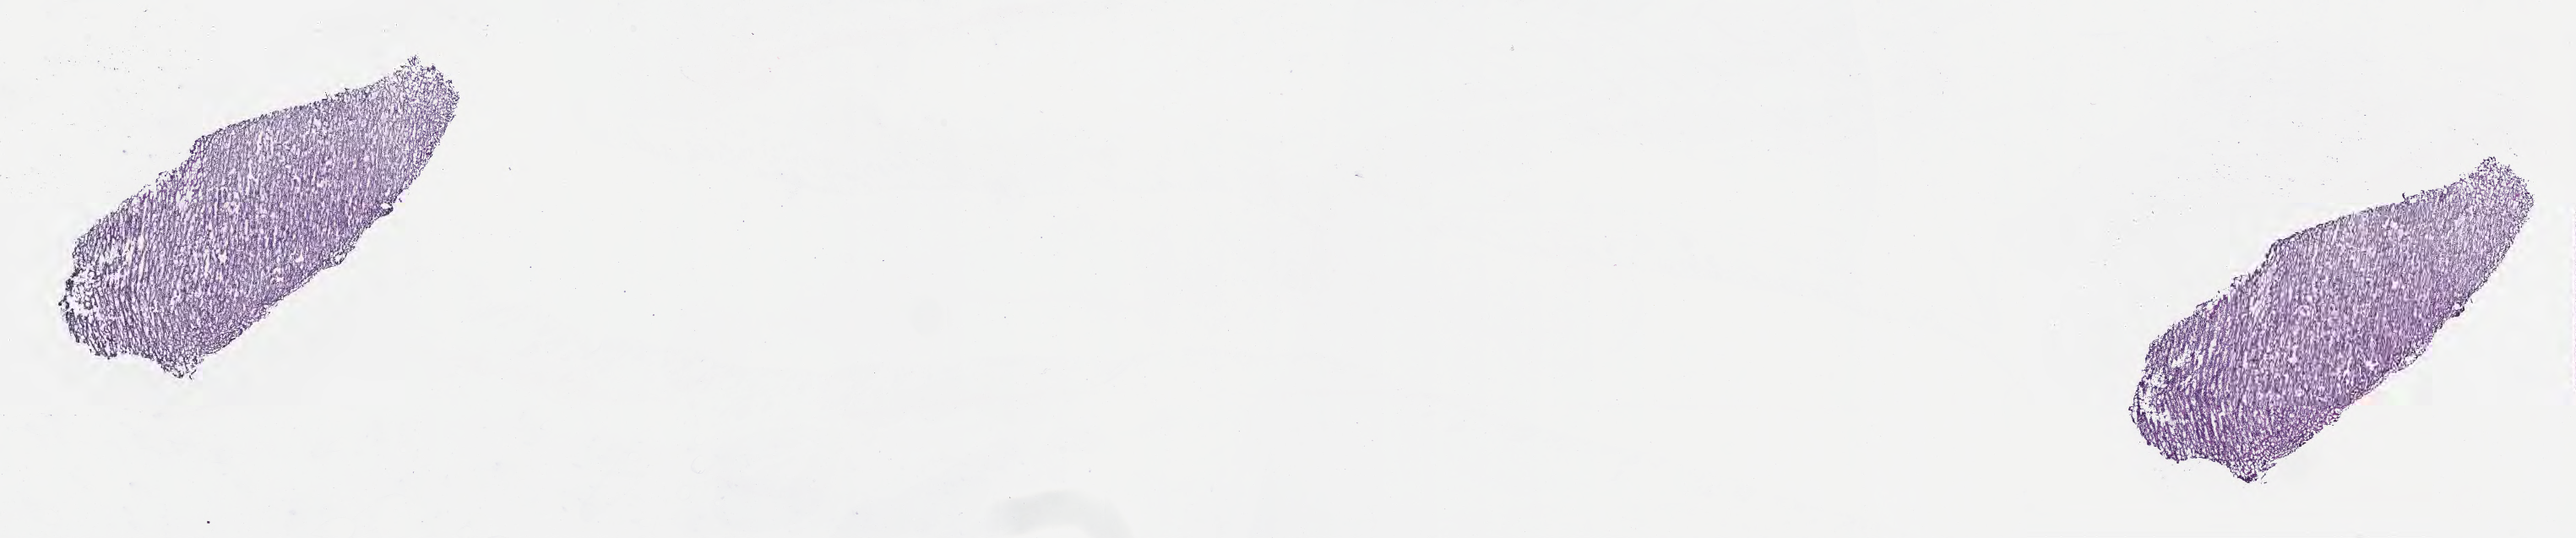
Digitized haematoxylin and eosin-stained section of tumor tissue from the adrenal gland — whole scanned area (about 24.7 x 5.1 mm) shown as a low-resolution overview, cryosection (OCT / tissue freezing medium). Patient female; age 69 months (5 years 9 months).
- diagnosis (ICD-O-3 morphology term): Neuroblastoma, NOS